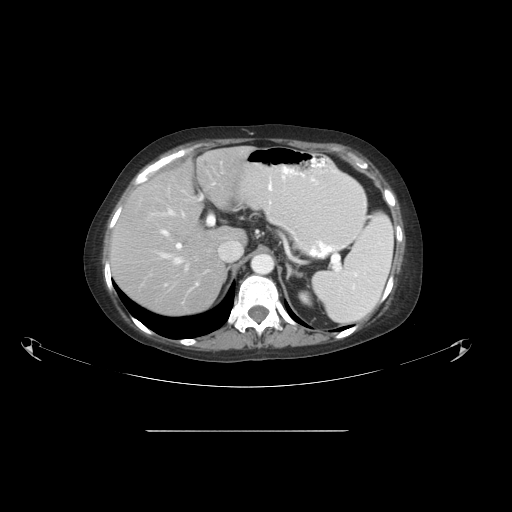
Contrast-enhanced abdominal CT, one axial slice; slice 36 of 51 in the series (ordered by position); reconstruction kernel STANDARD; 120 kVp; soft-tissue window (W 400 / L 40 HU); 5 mm slice thickness; 512 × 512 image matrix, field of view 475 × 475 mm. Female patient, age 48 years. Case-level facts recorded for this patient, not image findings: diagnosis: colorectal cancer liver metastases, imaged before liver resection; multiple liver metastases: yes.
Outlined on this slice (manually delineated by an expert):
- hepatic veins: bounding box [x1, y1, x2, y2] px = [148, 210, 242, 277]
- liver: [111, 148, 252, 317]
- planned liver remnant (the part of the liver to remain after resection): [111, 165, 234, 318]
- portal vein (with intrahepatic branches): [160, 172, 223, 285]
- liver metastasis: [203, 160, 209, 164]